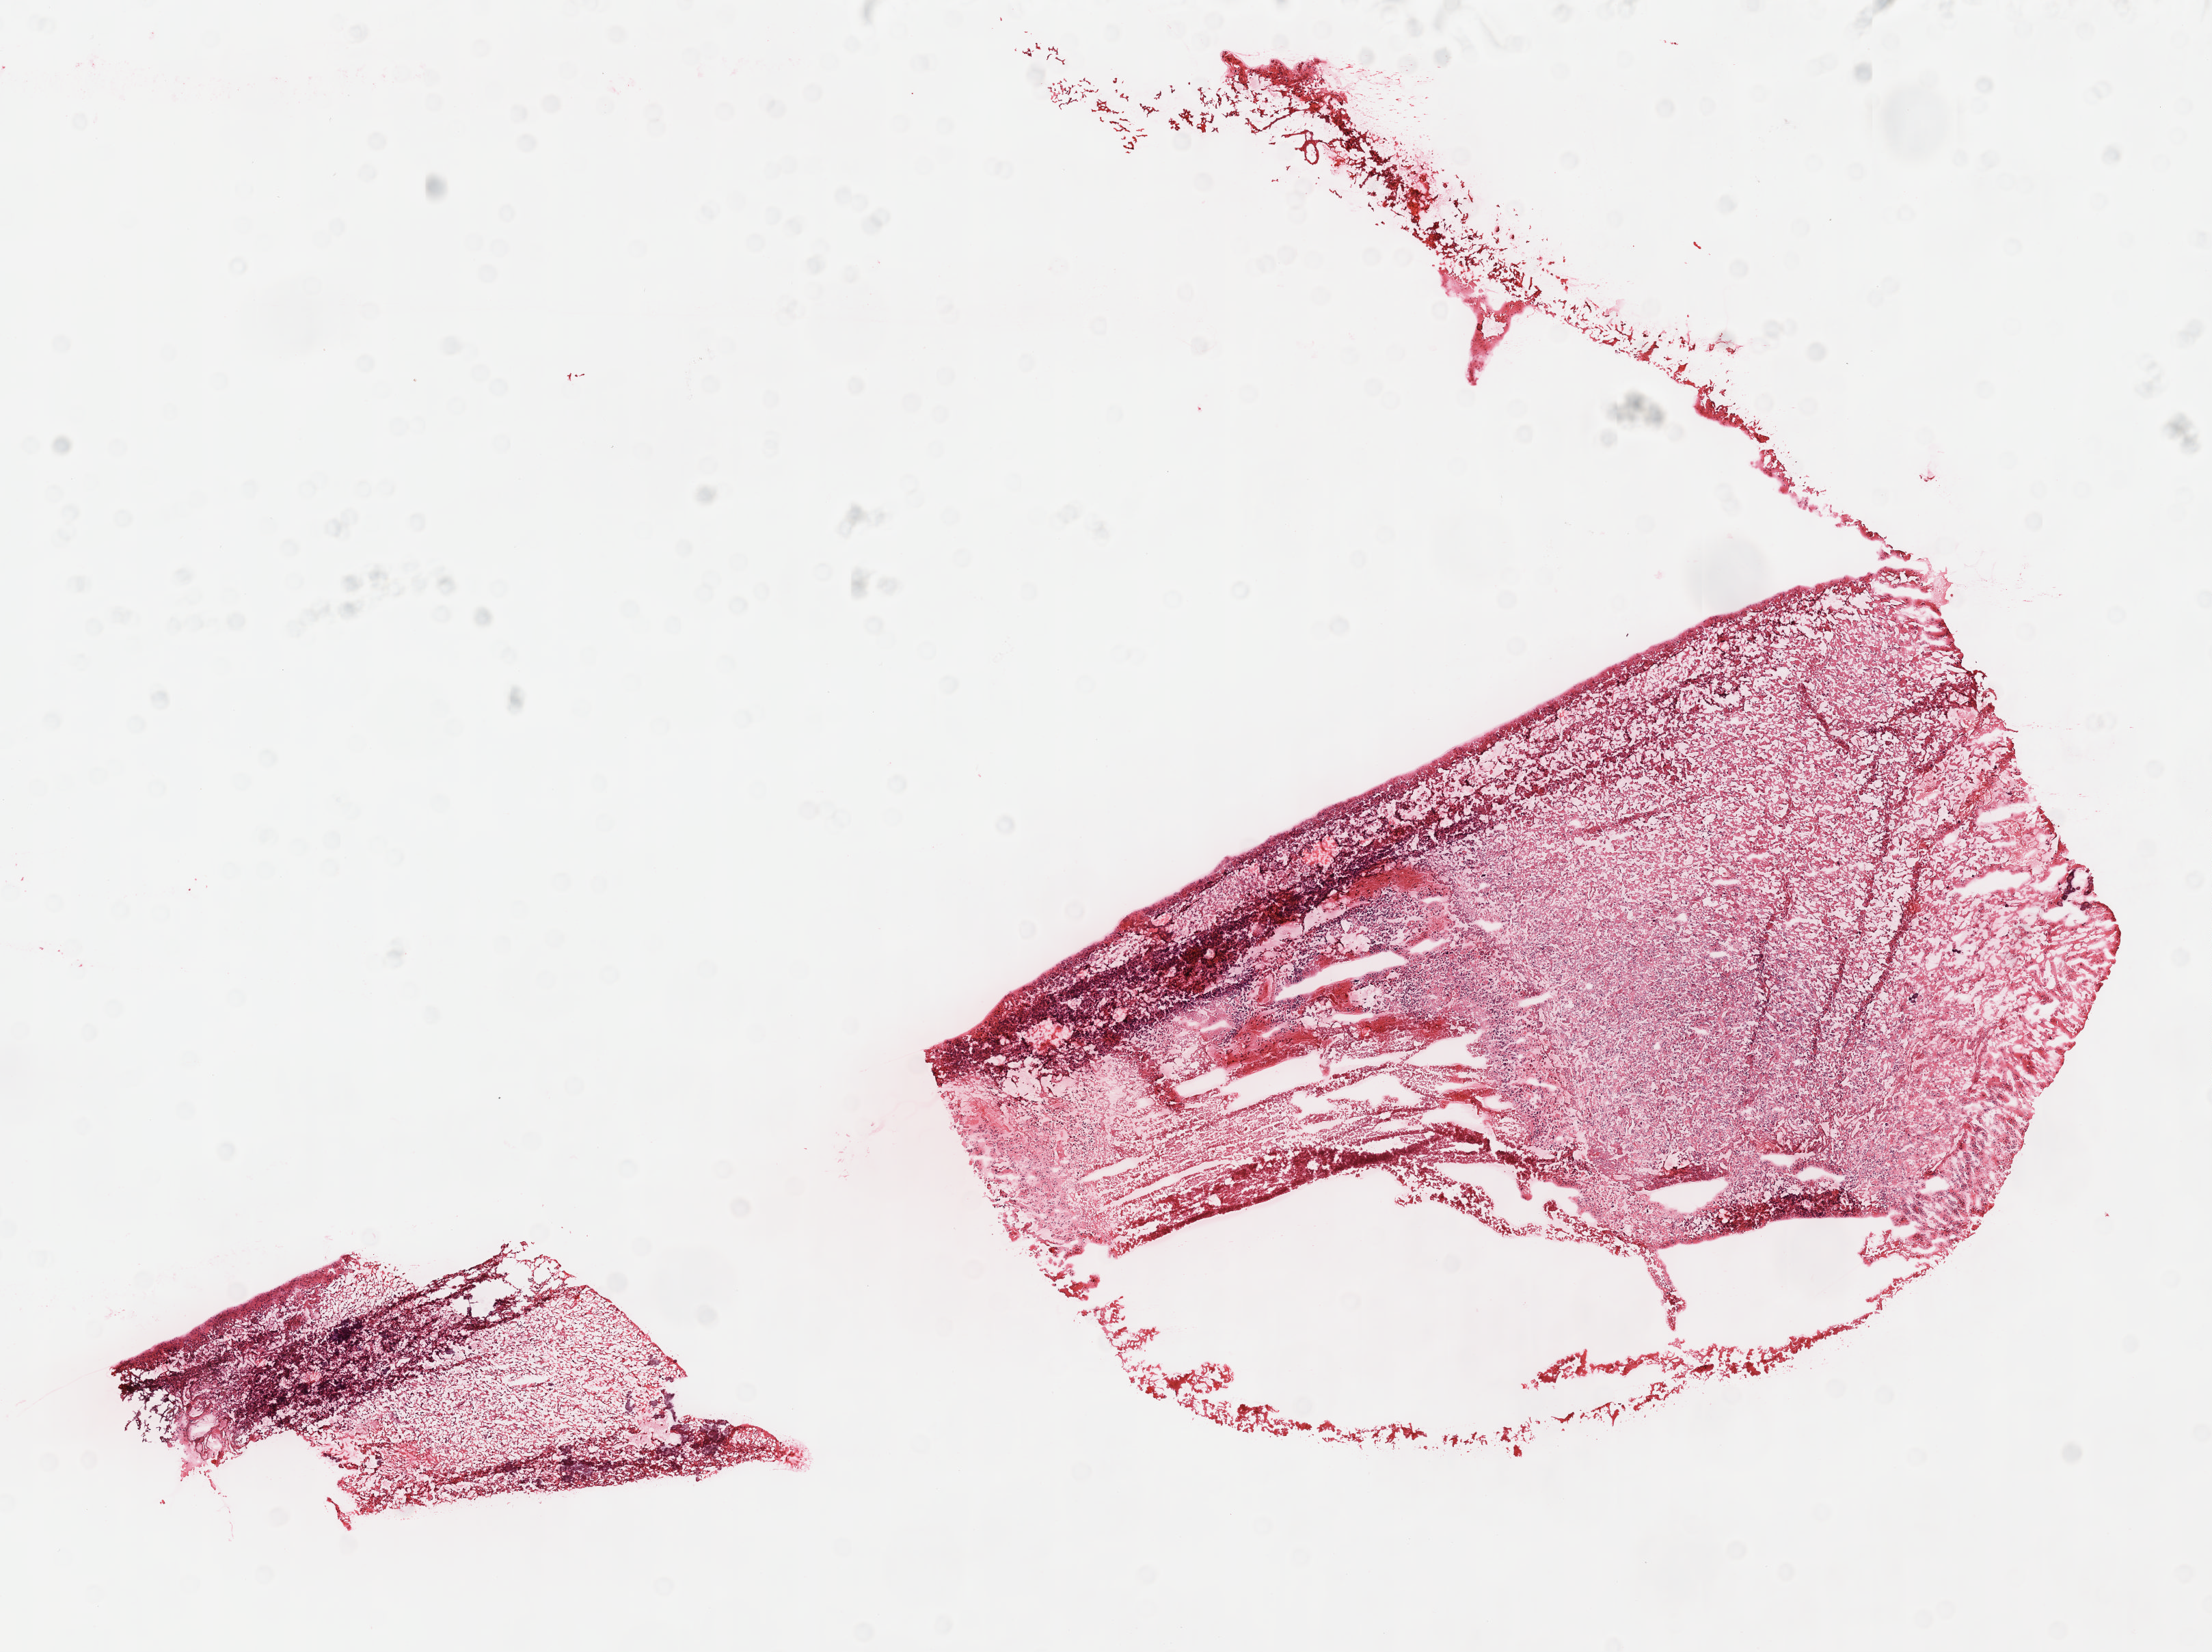
Digitized H&E tissue section (whole slide) — a low-resolution overview of the entire scanned area, about 13.1 x 9.8 mm. Frozen section from the top of the tissue portion. Brain, primary tumour sample. Female, age 38 years at initial diagnosis. Composition of this section per pathologist review: tumour cells 80%, tumour nuclei 100%, normal cells 0%, stromal cells 0%, necrosis 20%. Infiltration values recorded for this section: lymphocyte infiltration 0%.
- pathologic diagnosis: Glioblastoma